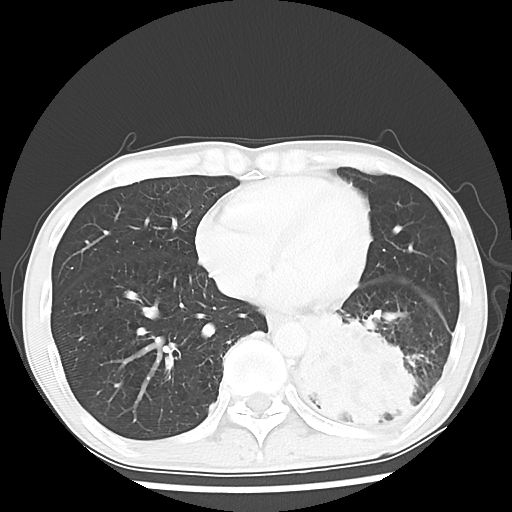
Chest CT, one axial slice. Slice 21 of 64 in the series (ordered by position). Reconstruction kernel LUNG. 120 kVp. Lung window (W 1500 / L -600 HU). 5 mm slice thickness. 512 × 512 image matrix. Patient: male, 68 years. Case-level facts recorded for this patient, not image findings: clinical TNM (as recorded): T4 N0 M0.
Annotated regions visible in this slice (bounding box drawn by a radiologist):
- lung tumour (recorded histology: squamous cell carcinoma): bounding box [x1, y1, x2, y2] px = [289, 316, 448, 445]